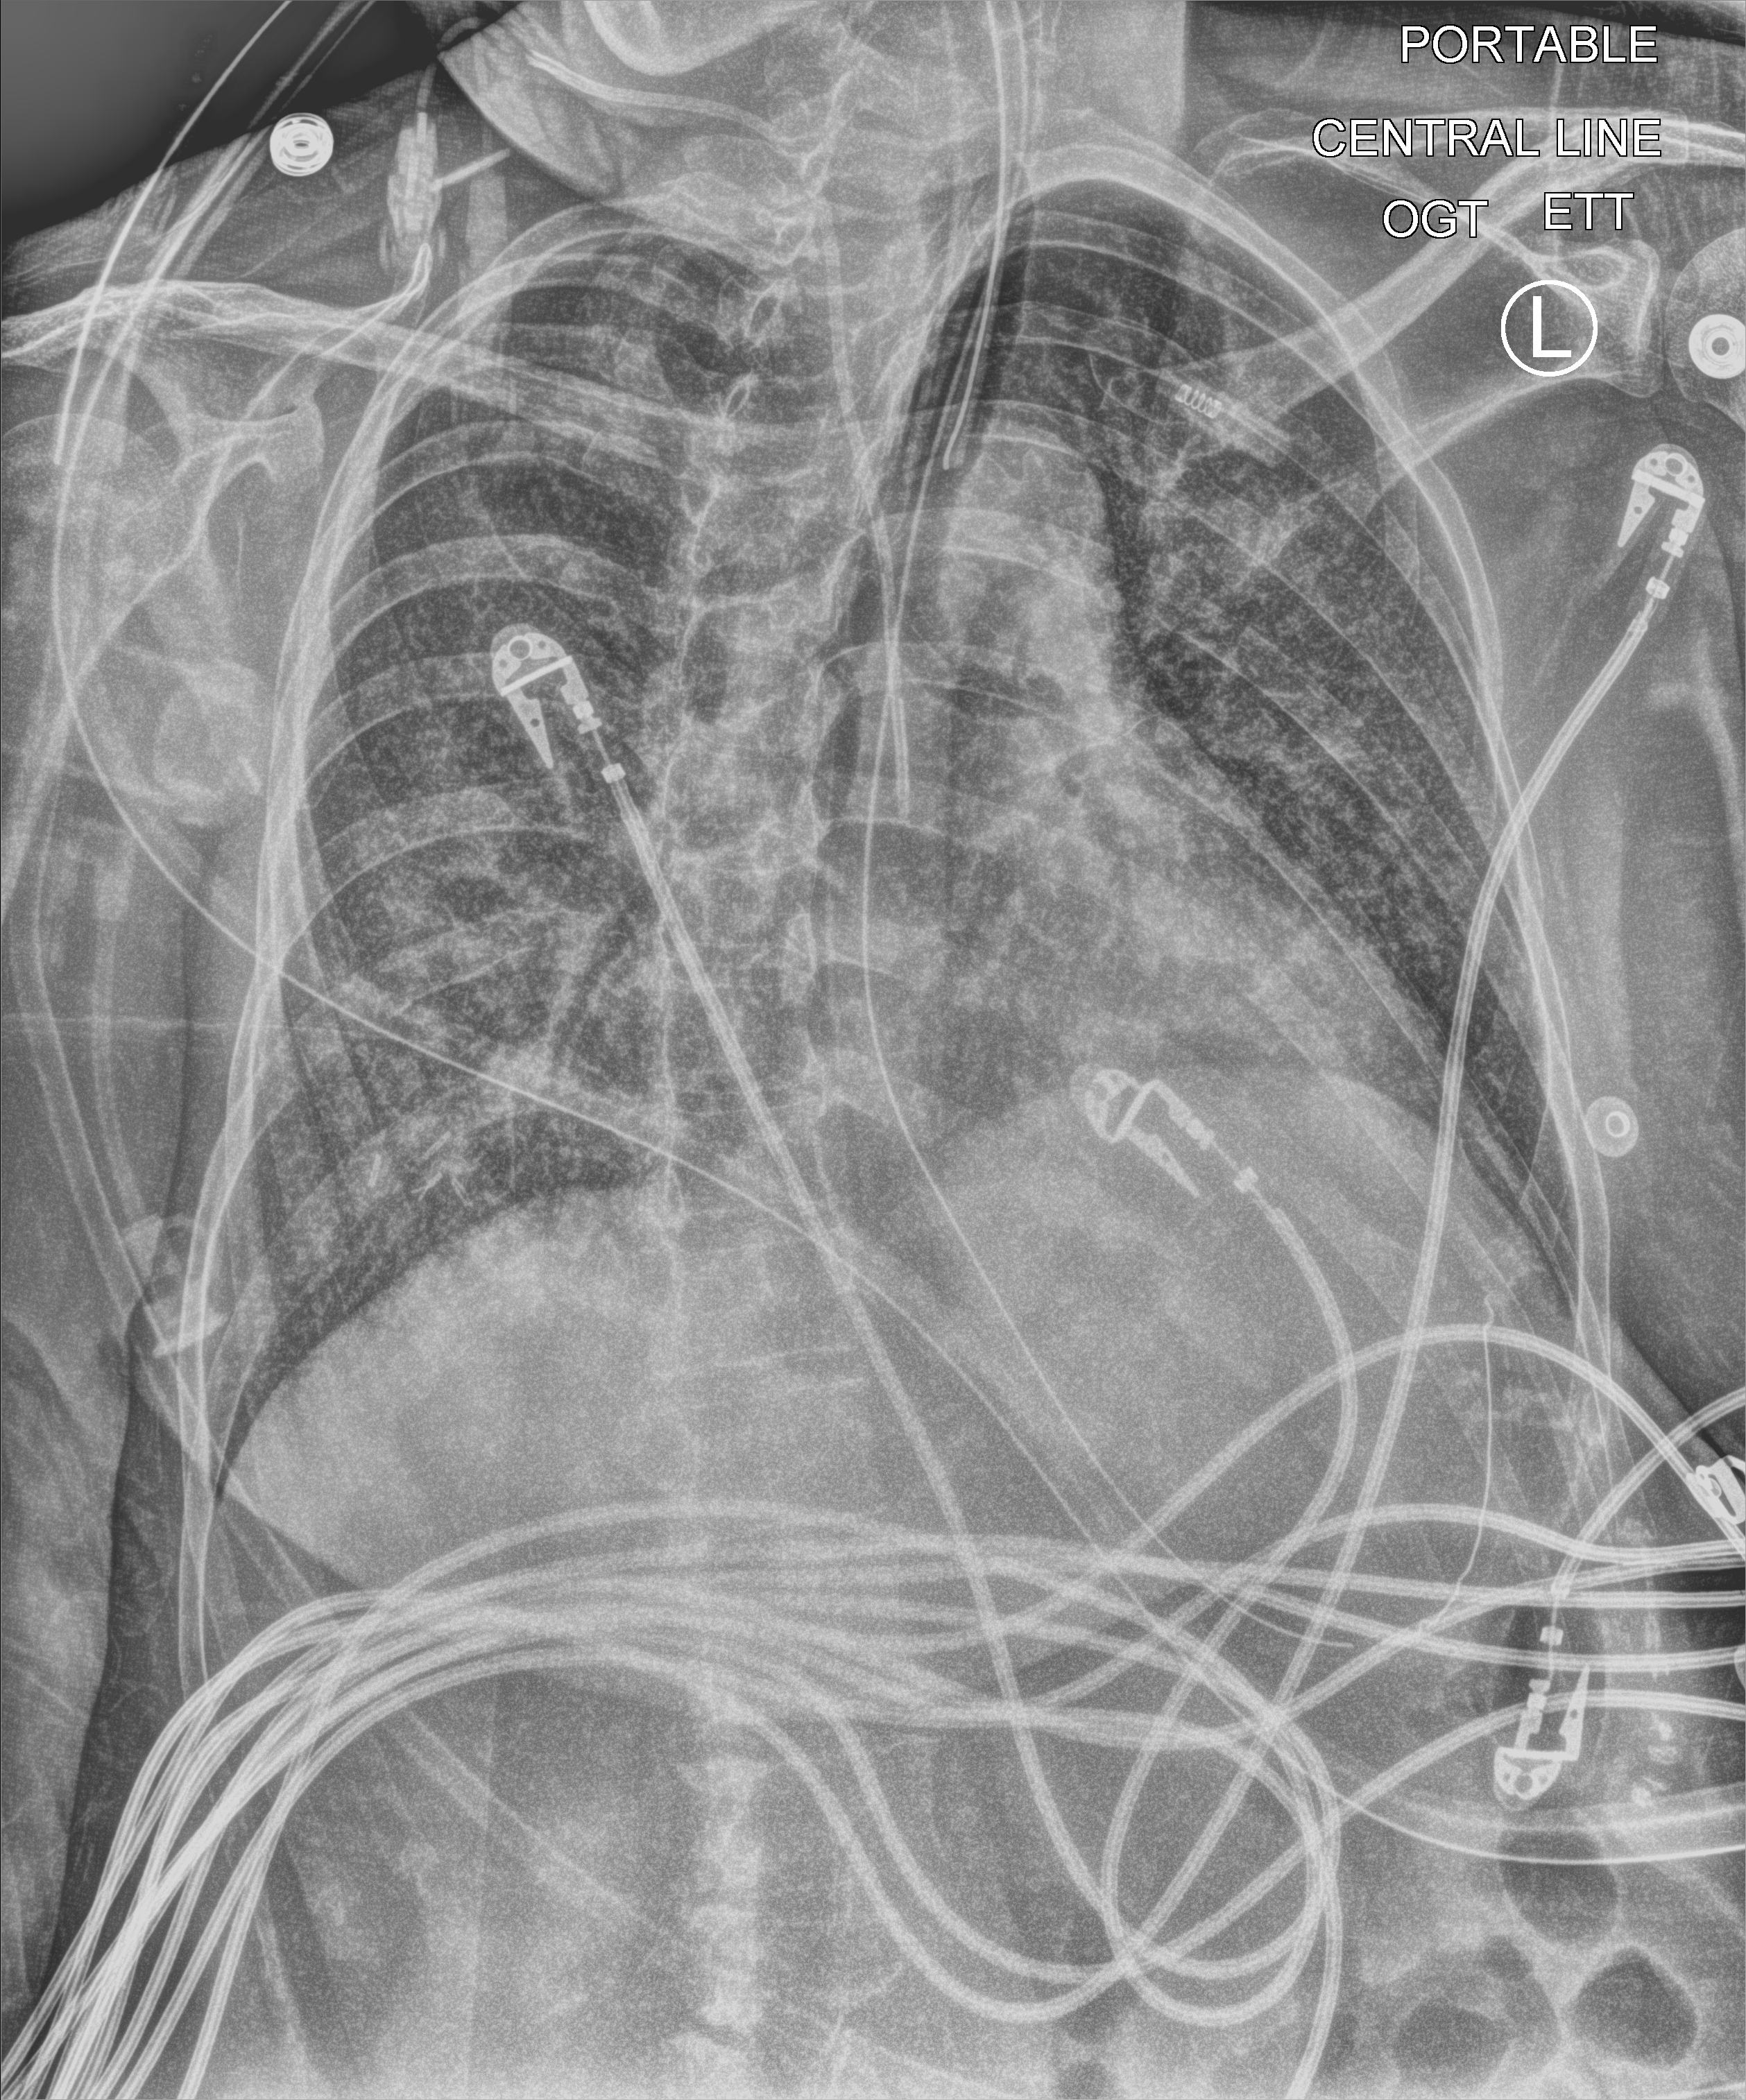
Bedside chest radiograph (computed radiography), anteroposterior (AP) projection. Patient hospitalised with COVID-19; female, aged 18–59 years.
From the hospital-stay record, not from the radiograph (when in the stay this image was taken is not recorded): hypertension (admission record): no; smoking status (admission record): never; admitted to intensive care during this hospital stay: no.